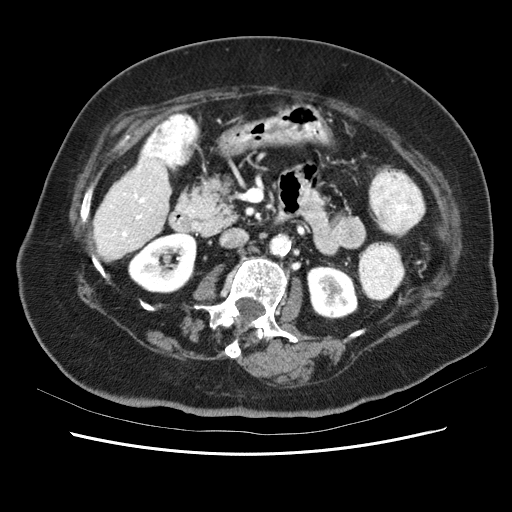
Contrast-enhanced abdominal CT (liver protocol), one axial slice; position 16 of 62 along the scan axis; reconstruction kernel STANDARD; 120 kVp; soft-tissue window (W 400 / L 40 HU); 2.5 mm slice thickness; 512 × 512 image matrix, field of view 340 × 340 mm. Case-level facts recorded for this patient, not image findings: diagnosis: hepatocellular carcinoma (patient treated with transarterial chemoembolisation; whether this scan precedes or follows treatment is not stated here); TNM stage (as recorded): Stage-I; Child-Pugh class: B; tumour nodularity: uninodular.
Outlined on this slice (semi-automatic segmentation, software-assisted and operator-edited):
- liver parenchyma outside the tumour (the mass and vessels are separate outlines, so this box may not span the whole liver): bounding box [x1, y1, x2, y2] px = [92, 148, 171, 266]
- liver vessels: [95, 153, 167, 256]